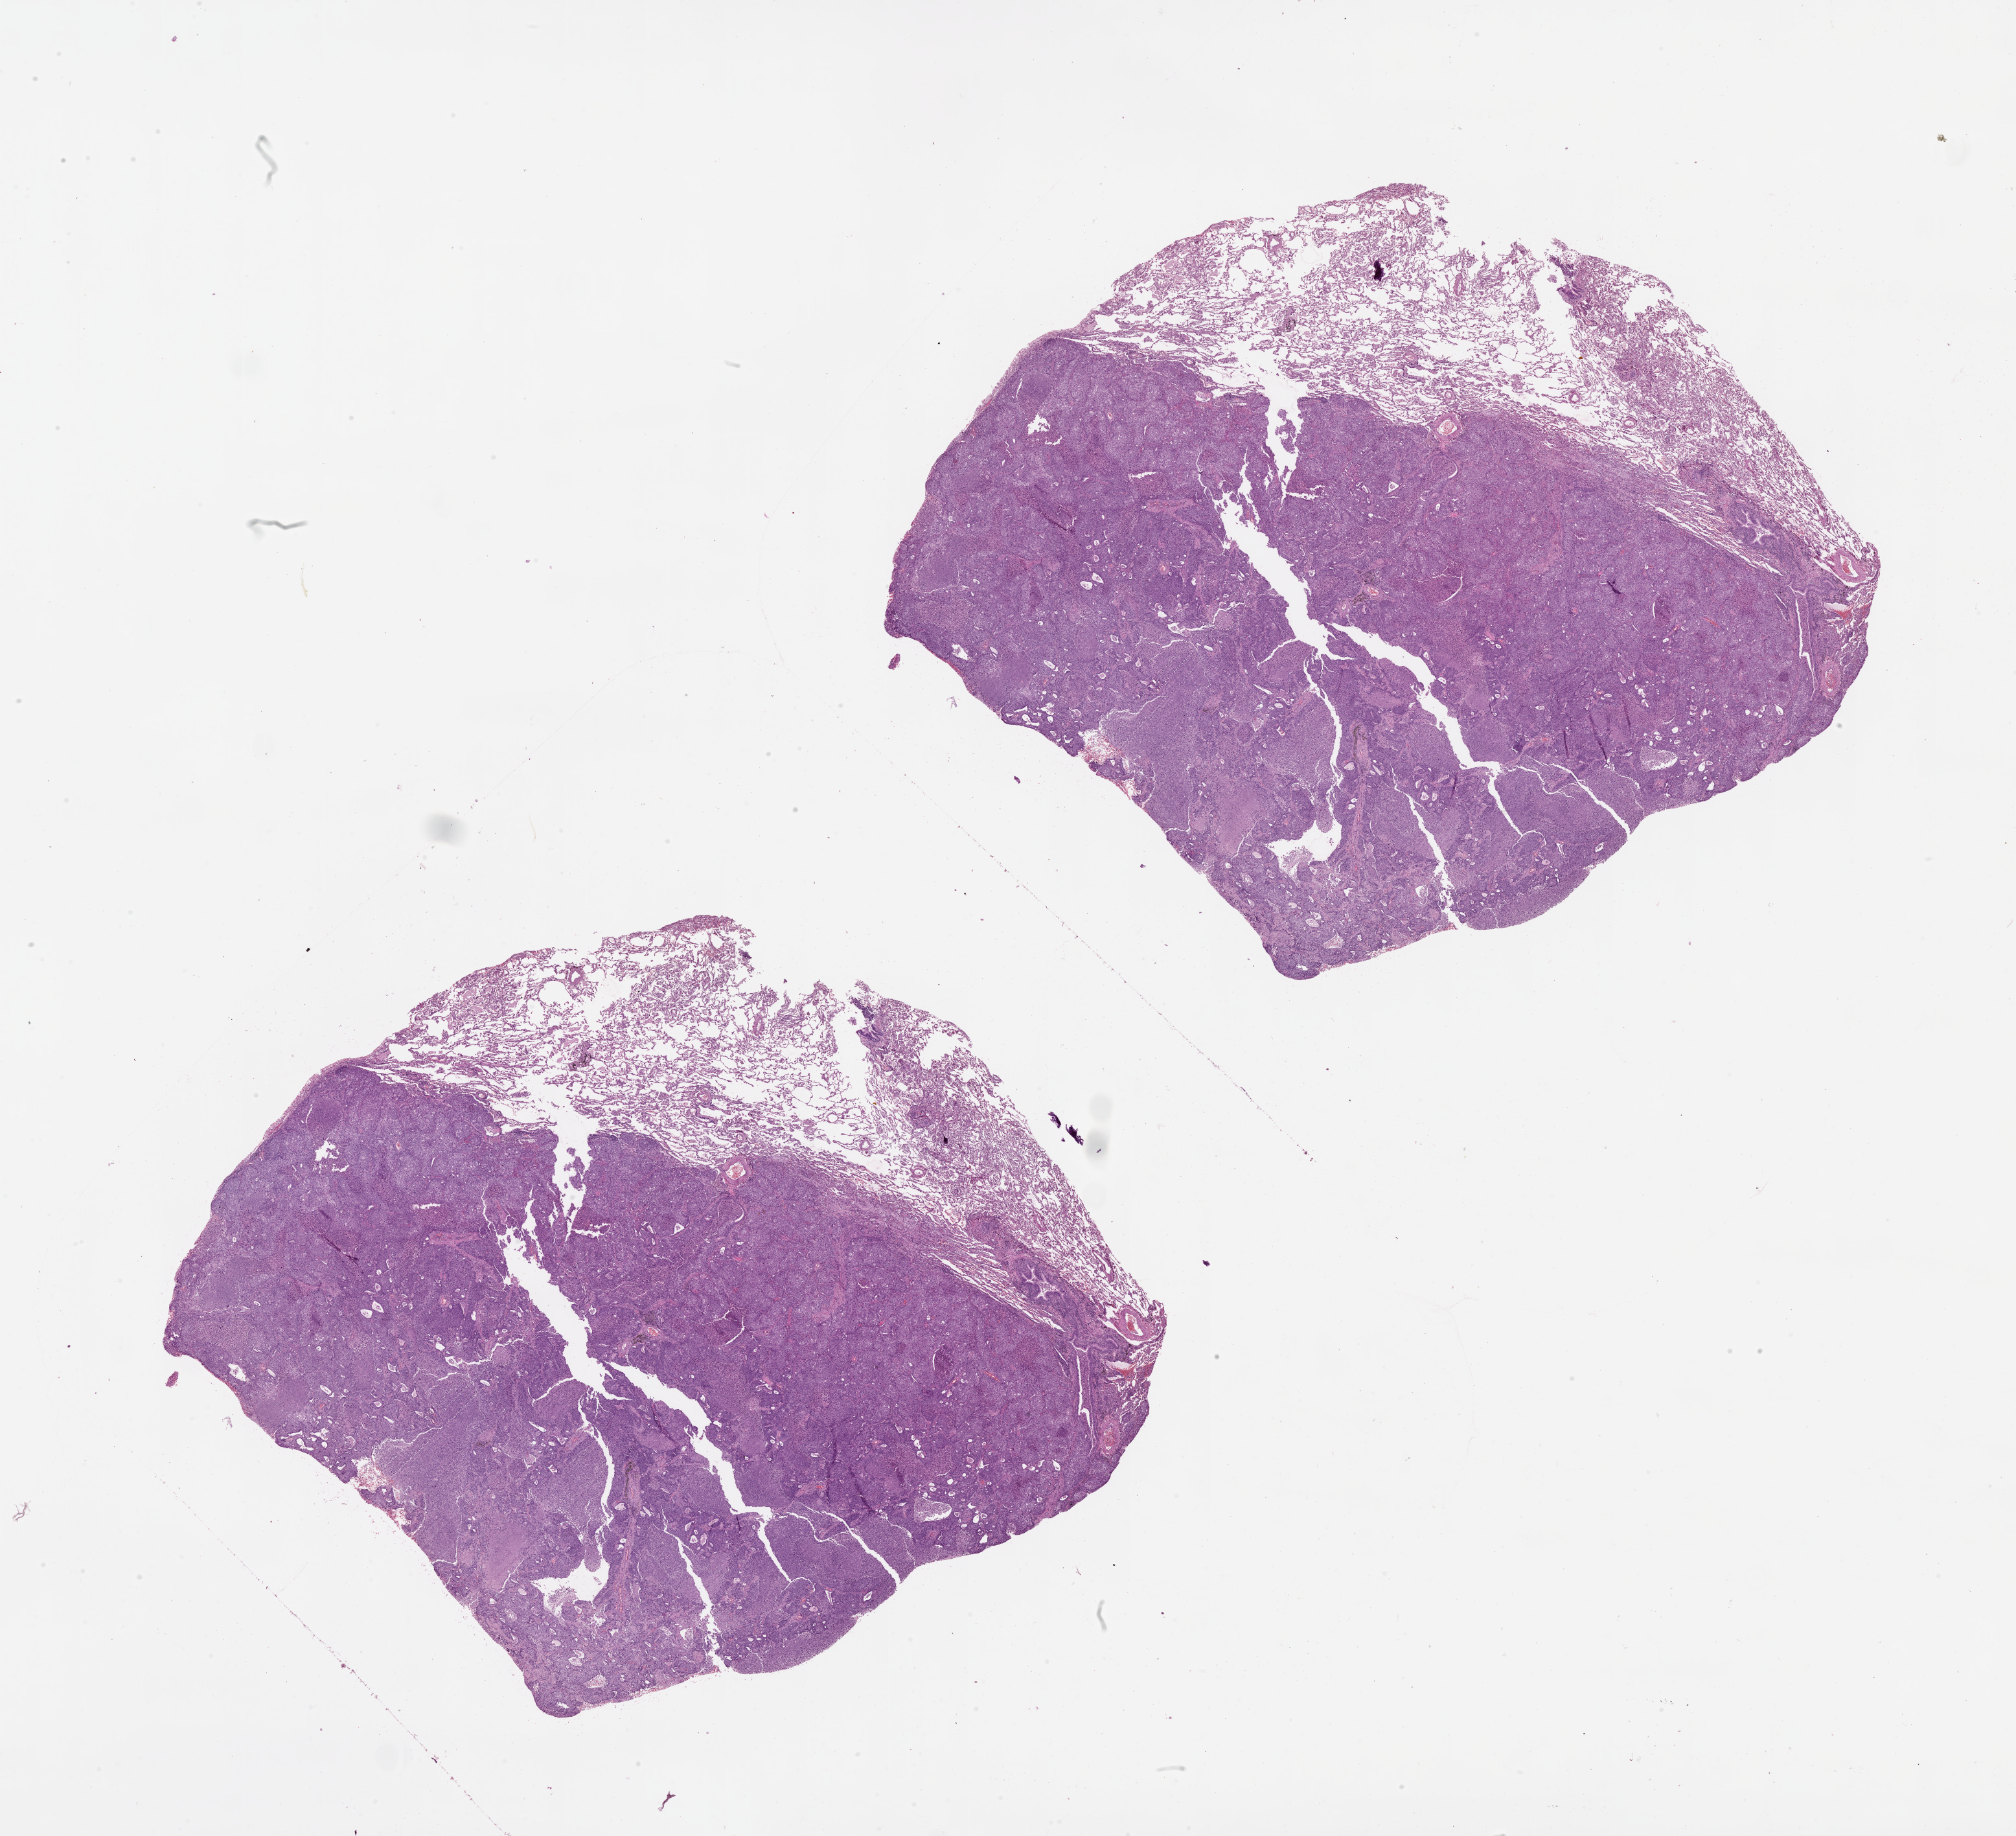
Digitized H&E tissue section (whole slide), a low-resolution overview of the entire scanned area, about 25.1 x 22.8 mm (slide scanned at 20x); lung, tumour tissue. Male, 63 y/o.
• patient diagnosis (cohort enrolment): squamous cell carcinoma (lung)